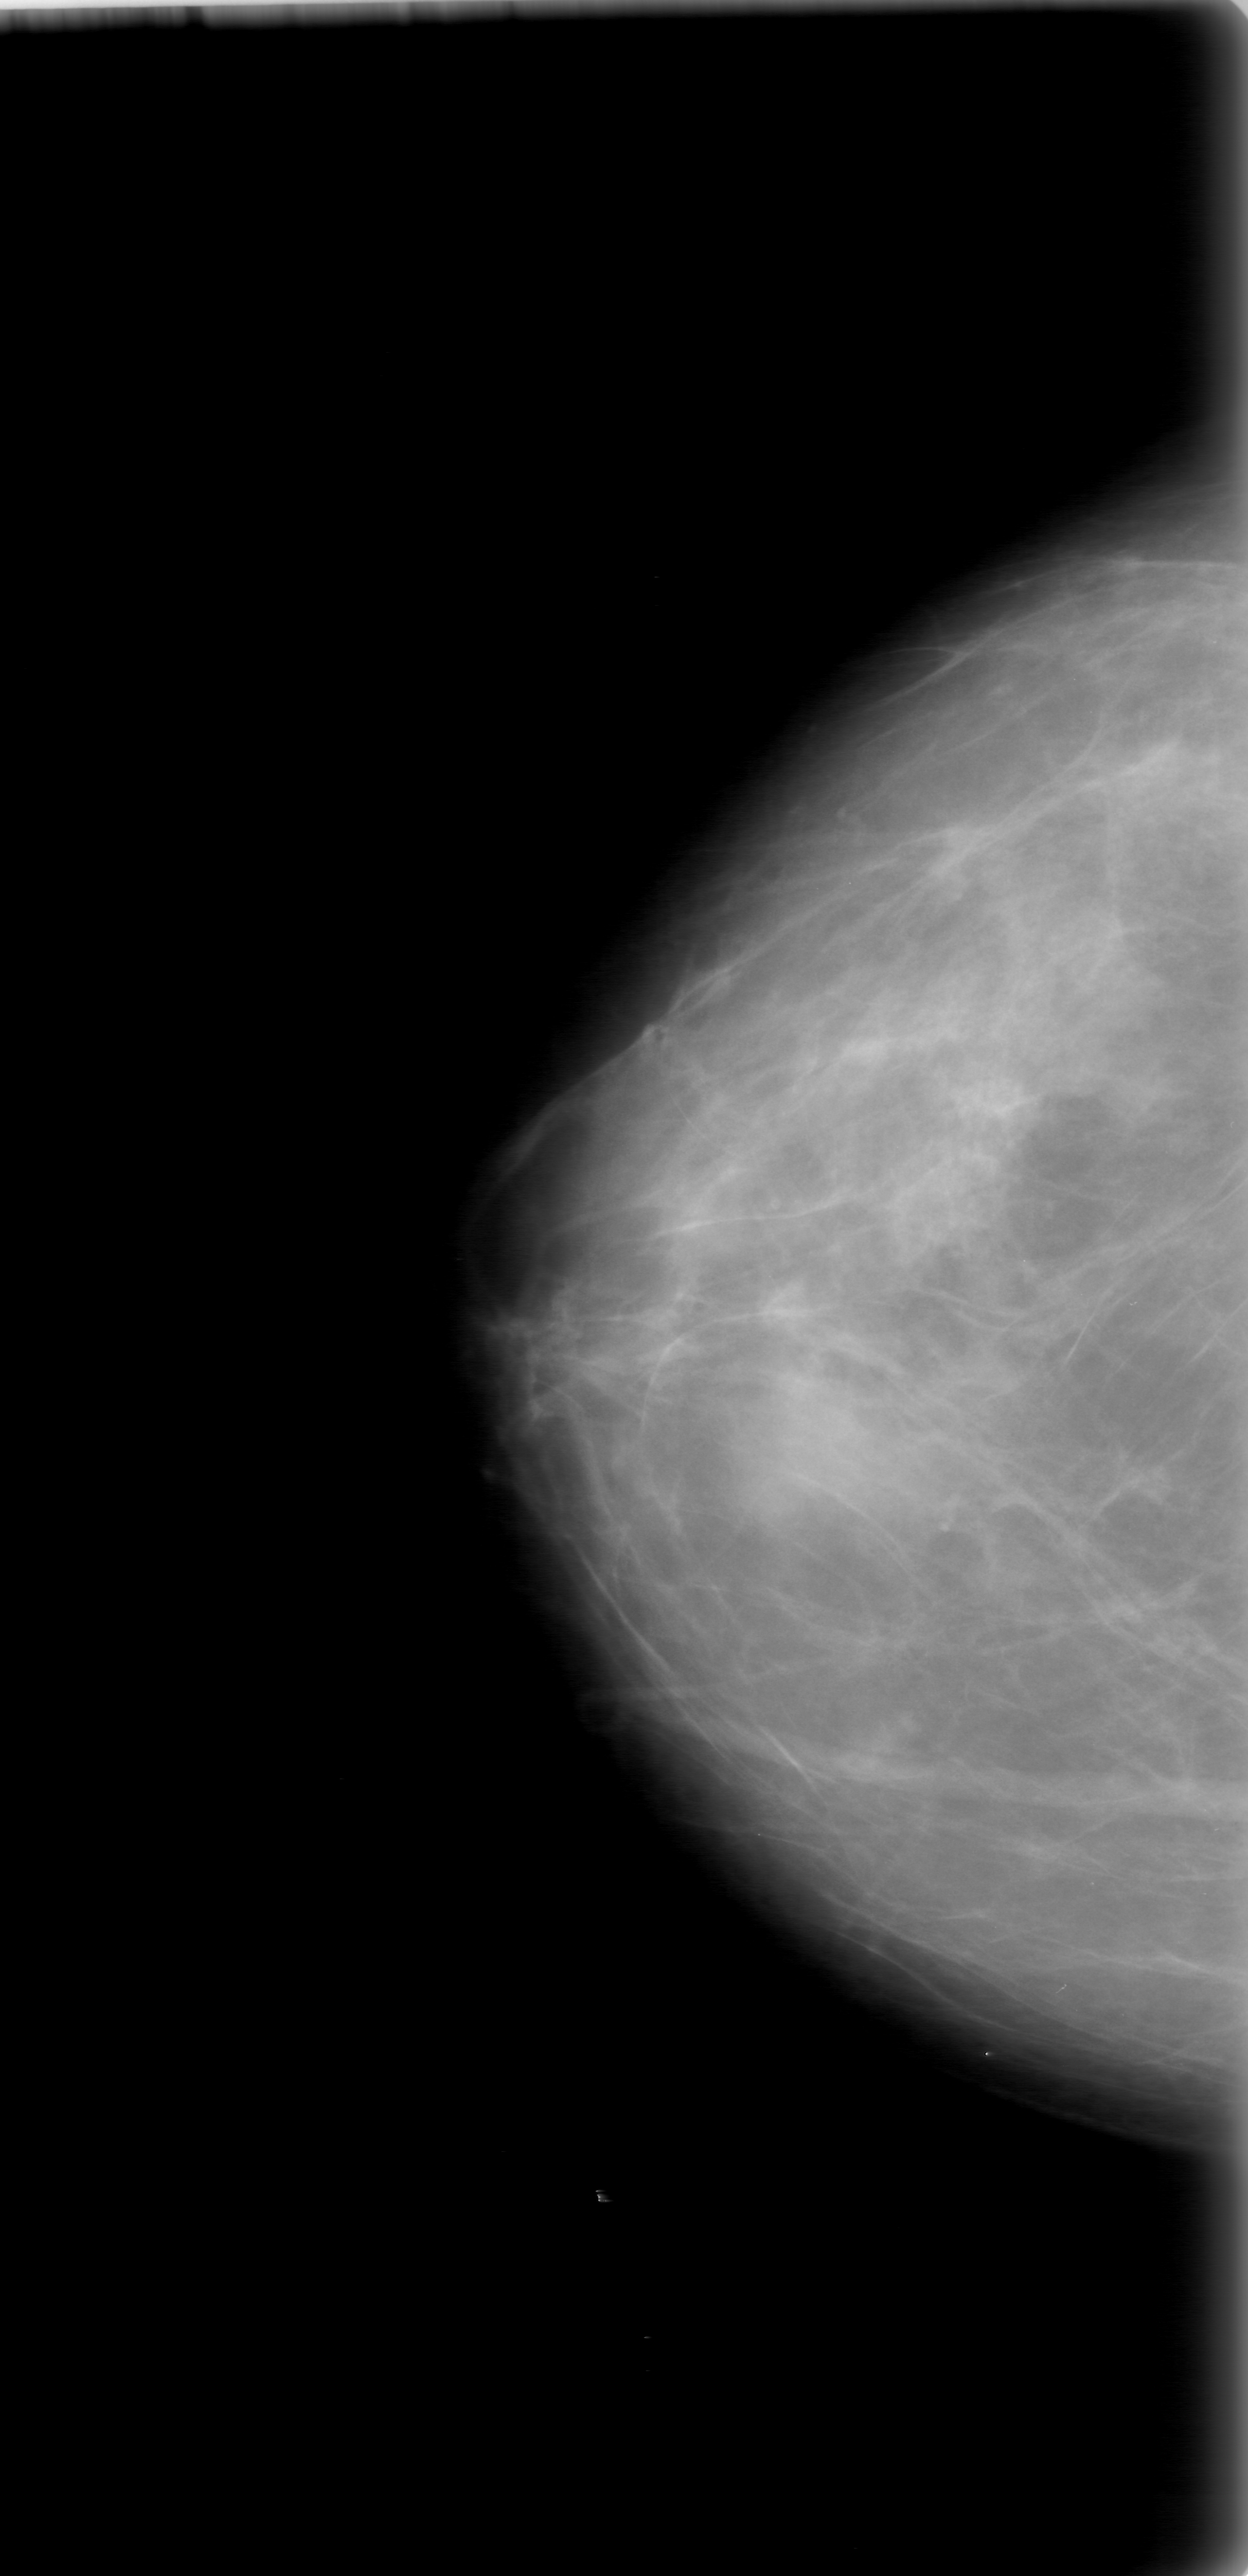
Mammogram (digitized film), right breast, craniocaudal (CC) view.
- Abnormality record for this image: mass, shape oval, margins obscured; BI-RADS assessment category 0 (incomplete: needs additional imaging); pathology (as recorded): benign.